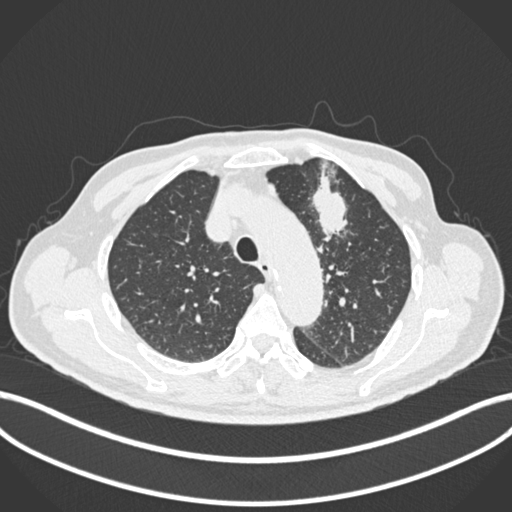
Chest CT, one axial slice. Slice 192 of 261 in the series (ordered by position). 120 kVp. Lung window (W 1500 / L -600 HU). 1 mm slice thickness. 512 × 512 image matrix, field of view 400 × 400 mm. Patient: male, 74 years. From the clinical record (not read from this slice): clinical TNM (as recorded): T2b N0 M1c.
Annotated regions visible in this slice (bounding box drawn by a radiologist):
- lung tumour (recorded histology: adenocarcinoma): bounding box (x1, y1, x2, y2) in pixels: (308, 168, 351, 244)